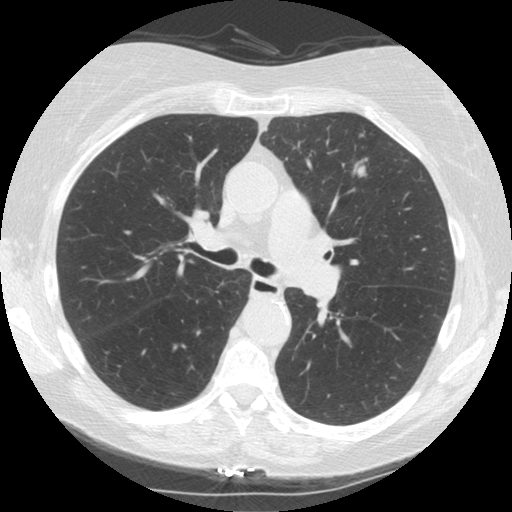
Low-dose screening chest CT, one axial slice. Position 91 of 153 along the scan axis. Reconstruction kernel STANDARD. 120 kVp. Lung window (W 1500 / L -600 HU). 2.5 mm slice thickness. 512 × 512 image matrix, field of view 330 × 330 mm.
Annotated regions visible in this slice (outlined manually by an expert reader):
- lesion 1 (tumor, upper lobe of left lung): bounding box (x1, y1, x2, y2) in pixels: (357, 166, 365, 176)